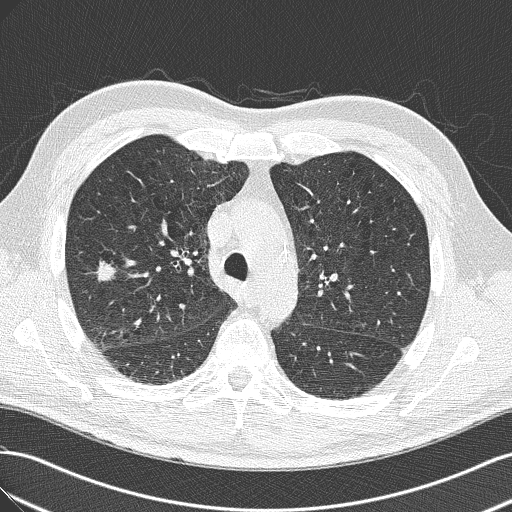
Low-dose screening chest CT, one axial slice; reconstruction kernel B50f; 120 kVp; lung window (W 1500 / L -600 HU); 512 × 512 image matrix.
Outlined on this slice (manually delineated by an expert):
- lesion 1 (tumor, lower lobe of right lung): bounding box <96,261,116,281> (left, top, right, bottom; pixels)